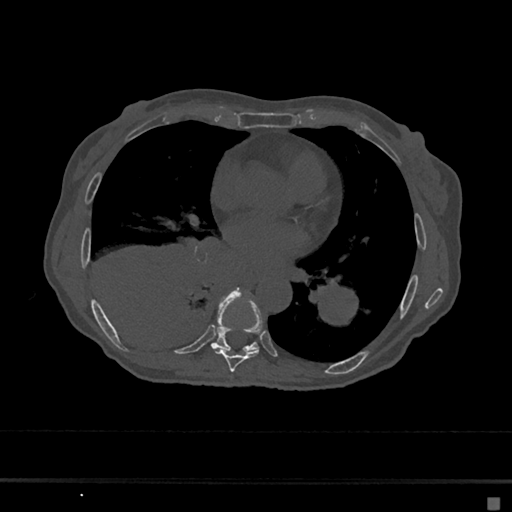
CT including the spine, one axial slice. Slice 351 of 797 in the series (ordered by position). 120 kVp. Bone window (W 1800 / L 400 HU). 512 × 512 image matrix, field of view 360 × 360 mm. Patient: female, 68 years. Case-level facts recorded for this patient, not image findings: primary cancer: renal.
Structures marked on this image (semi-automatic segmentation, software-assisted and operator-edited):
- T7 vertebra: box from (x=214, y=299) to (x=263, y=372) px
- T8 vertebra: (x=211, y=289)–(x=258, y=353)